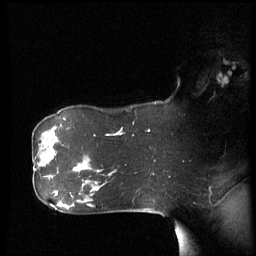
Breast MRI (dynamic contrast-enhanced), one sagittal slice; position 42 of 60 along the scan axis; dynamic contrast-enhanced series, image 2 of 3 at this slice position (ordered by acquisition); 1.5 T; TE 4.2 ms, TR 8.4 ms; 2.9 mm slice thickness; 256 × 256 image matrix, field of view 280 × 280 mm. Female patient, age 61 years. Case-level facts recorded for this patient, not image findings: setting: breast cancer imaged before/during neoadjuvant chemotherapy; receptor status: HR-positive, HER2-negative.
Annotated regions visible in this slice (semi-automatic segmentation, software-assisted and operator-edited):
- analysis volume of interest (the breast-tissue region the enhancement analysis was run in; not a lesion): bounding box <34,142,60,179> (left, top, right, bottom; pixels)
- tumour enhancement mask (voxels above the 70 % enhancement threshold inside the analysis volume of interest): <41,156,46,167>